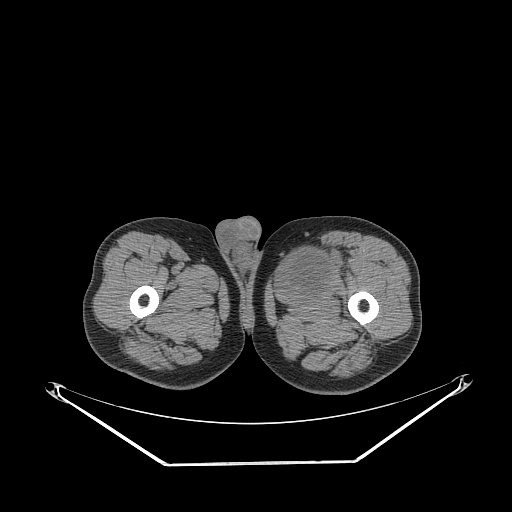
CT of an extremity soft-tissue mass (from a PET/CT study), one axial slice. Slice 261 of 267 in the series (ordered by position). 140 kVp. Soft-tissue window (W 400 / L 40 HU). 3.75 mm slice thickness. 512 × 512 image matrix, field of view 500 × 500 mm. Male patient. From the clinical record (not read from this slice): histological type: pleiomorphic liposarcoma; grade: high; site of the primary tumour: left thigh.
Outlined on this slice (expert contour drawn on MRI and transferred to this co-registered scan by the dataset authors):
- gross tumour volume including surrounding oedema: bounding box [x1, y1, x2, y2] px = [281, 242, 346, 296]
- gross tumour volume (mass): [281, 251, 330, 293]